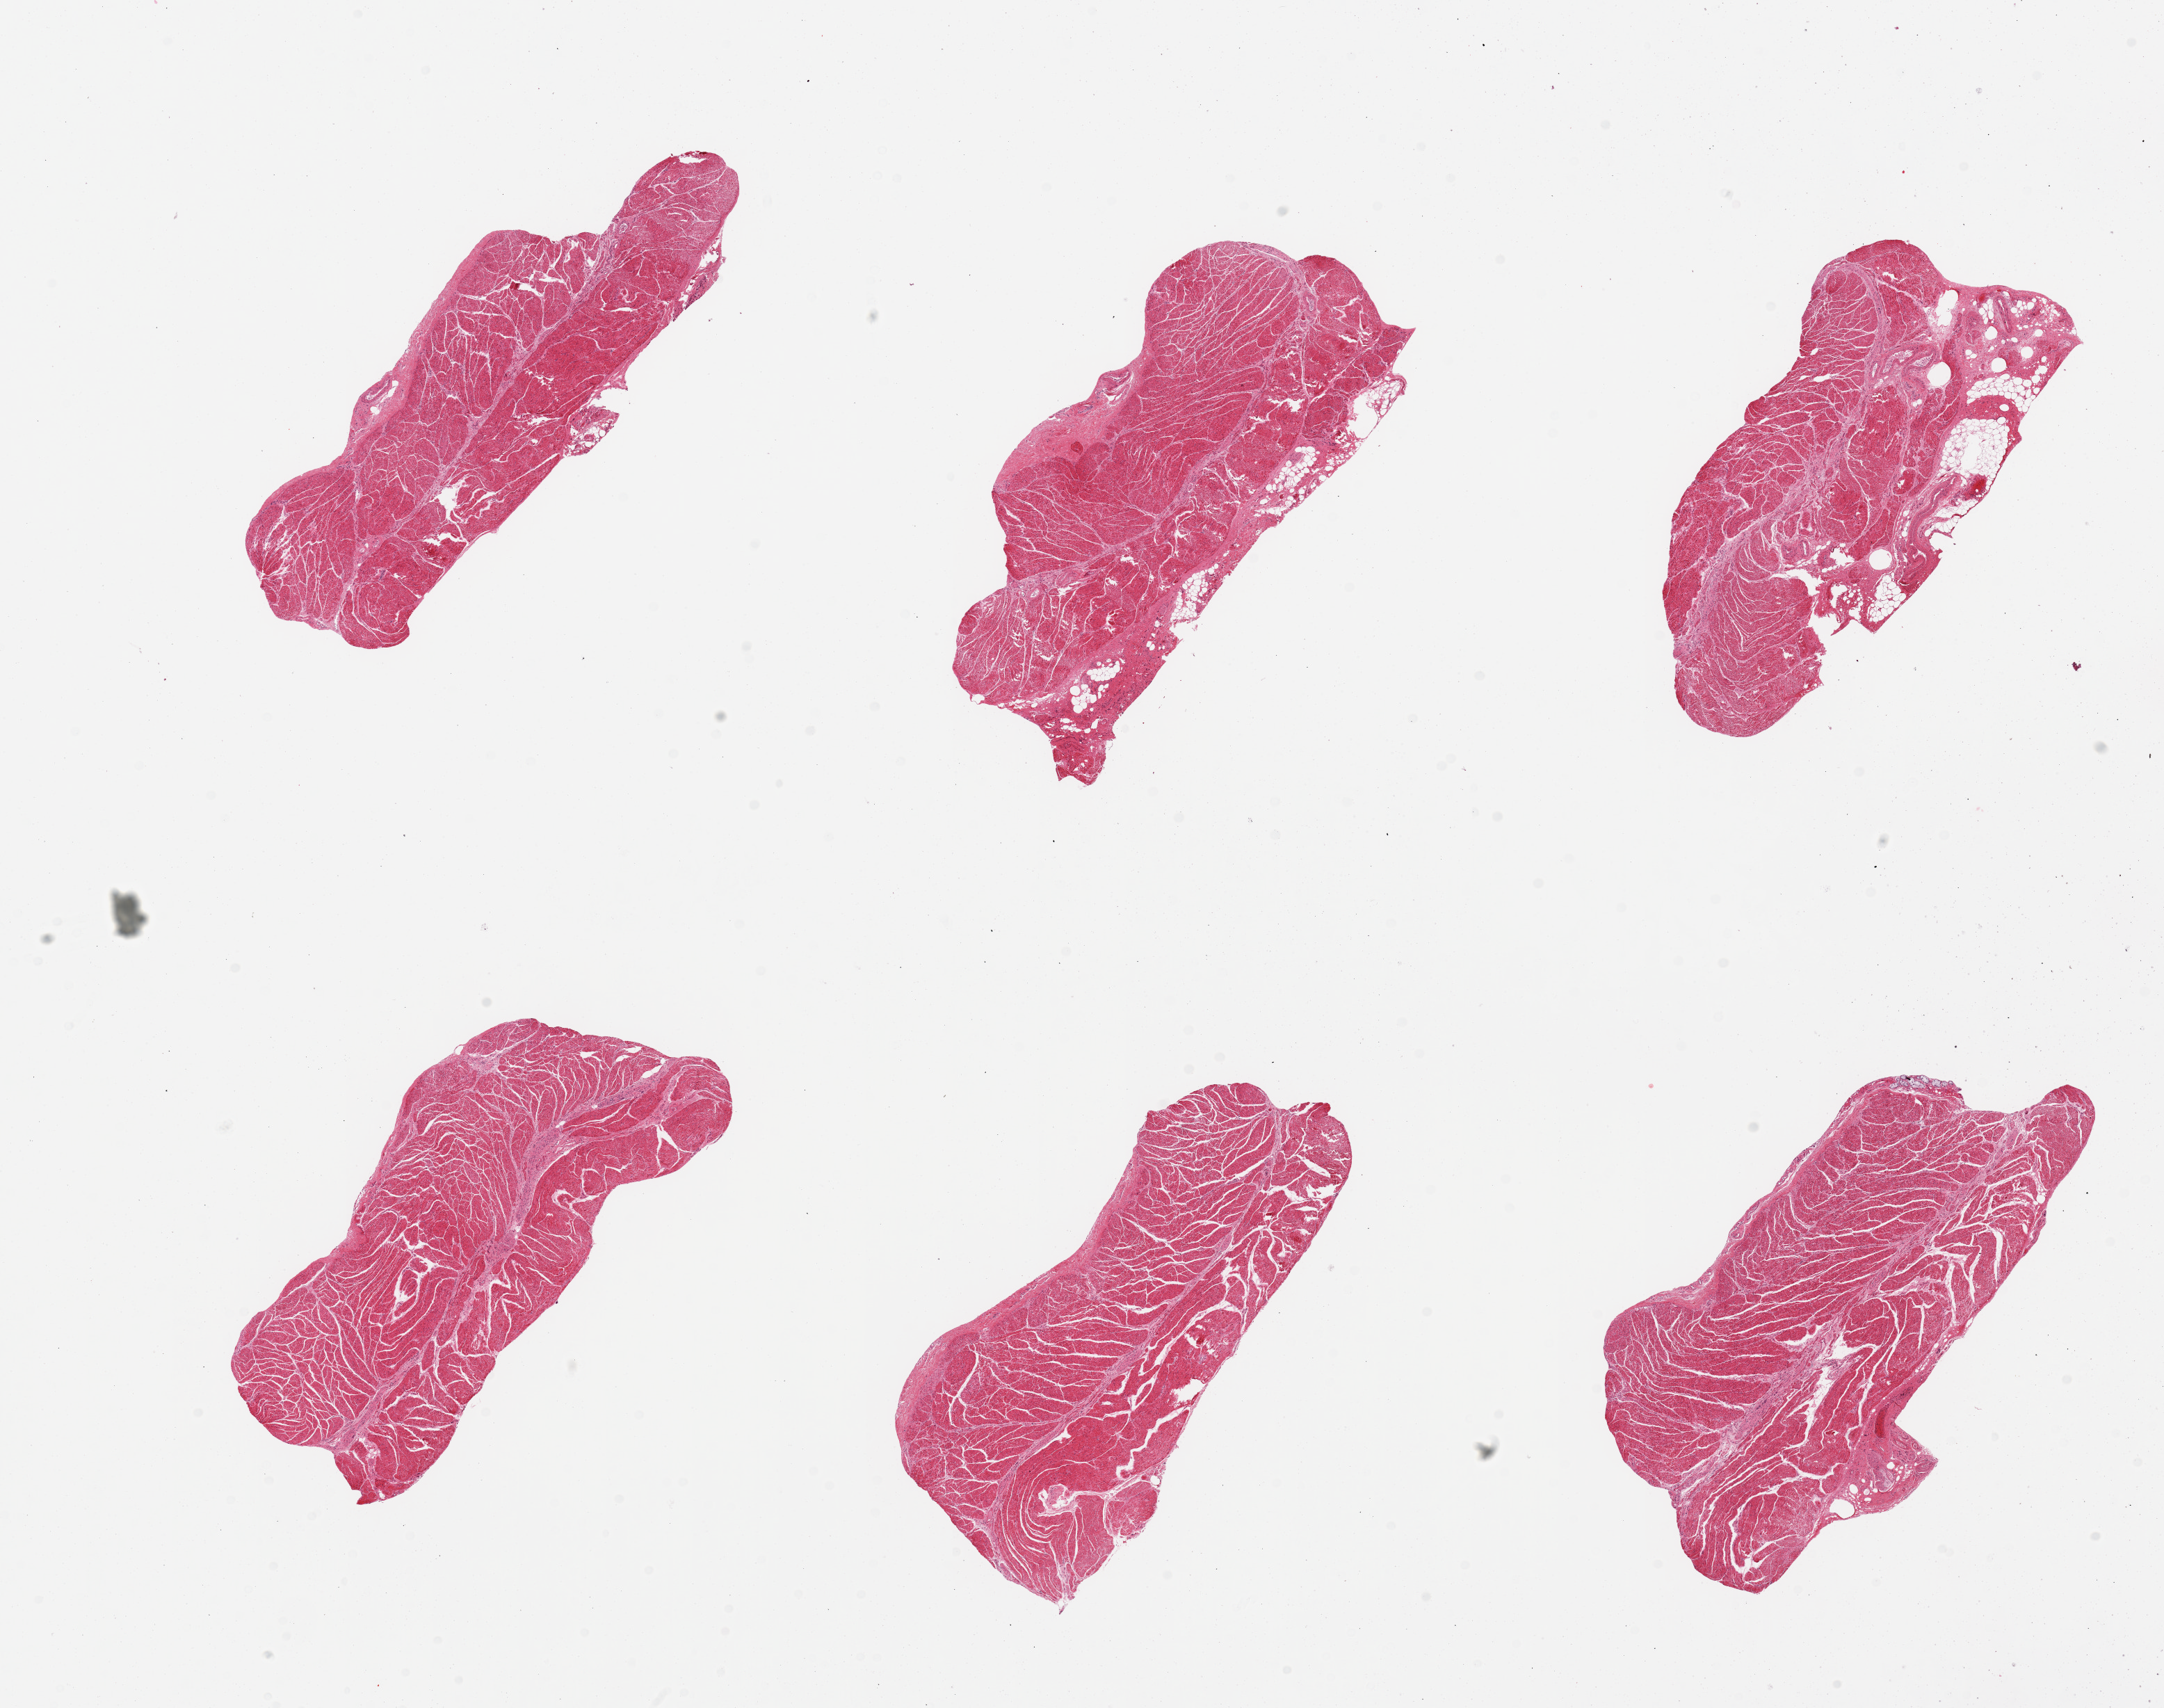
Digitized haematoxylin and eosin-stained section, low-resolution overview of the scanned area, about 24.6 x 19.4 mm; PAXgene-fixed paraffin-embedded (PFPE) section; target tissue: esophageal muscle; tissue donor sample. Donor: female.
Reviewer comment on this tissue sample: 6 pieces, few submucosal glands.